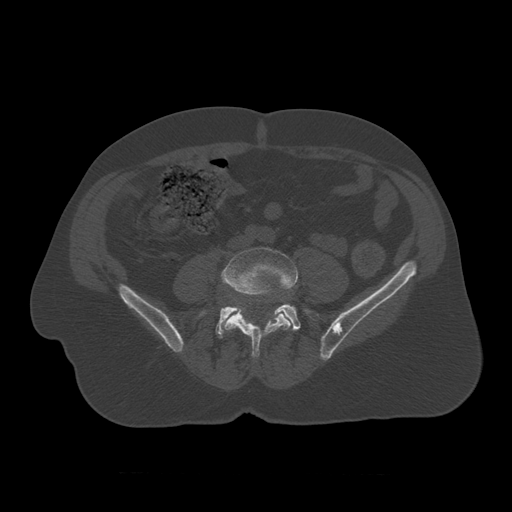
CT including the spine, one axial slice. Slice 267 of 450 in the series (ordered by position). Reconstruction kernel STANDARD. 120 kVp. Bone window (W 1800 / L 400 HU). 512 × 512 image matrix, field of view 405 × 405 mm. Patient age 75 years. From the clinical record (not read from this slice): primary cancer: prostate.
Structures marked on this image (semi-automatic segmentation, software-assisted and operator-edited):
- L4 vertebra: bounding box [x1, y1, x2, y2] px = [221, 248, 298, 358]
- L5 vertebra: [200, 297, 320, 339]